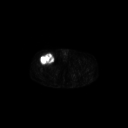
FDG PET of an extremity soft-tissue mass (from a PET/CT study), one axial slice; position 298 of 311 along the scan axis; 3.27 mm slice thickness; 128 × 128 image matrix, field of view 700 × 700 mm. Male patient, age 56 years. Case-level facts recorded for this patient, not image findings: histological type: pleiomorphic leiomyosarcoma; grade: intermediate; site of the primary tumour: right thigh.
Annotated regions visible in this slice (expert contour drawn on MRI and transferred to this co-registered scan by the dataset authors):
- gross tumour volume including surrounding oedema: bounding box (x1, y1, x2, y2) in pixels: (40, 53, 54, 65)
- gross tumour volume (mass): (40, 53, 54, 65)